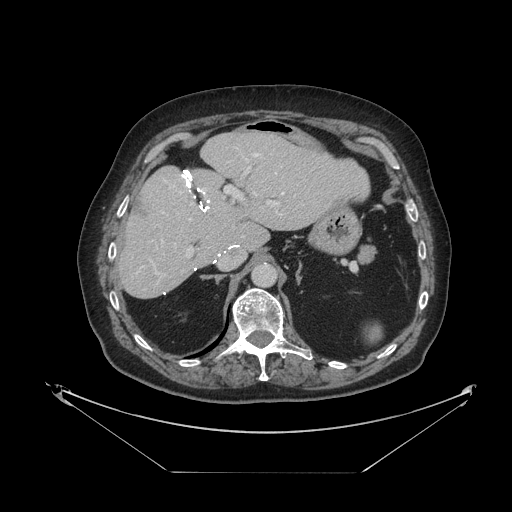
Contrast-enhanced abdominal CT, one axial slice. Position 69 of 121 along the scan axis. Reconstruction kernel STANDARD. 120 kVp. Intravenous contrast given. Soft-tissue window (W 400 / L 40 HU). 512 × 512 image matrix, field of view 500 × 500 mm. Male patient, age 68 years. Case-level facts recorded for this patient, not image findings: diagnosis: colorectal cancer liver metastases, imaged before liver resection; multiple liver metastases: no; largest metastasis: 4 cm.
Structures marked on this image (outlined manually by an expert reader):
- hepatic veins: bounding box [x1, y1, x2, y2] px = [162, 153, 284, 243]
- liver: [120, 133, 368, 299]
- planned liver remnant (the part of the liver to remain after resection): [120, 133, 368, 299]
- portal vein (with intrahepatic branches): [155, 168, 281, 274]
- liver metastasis: [131, 198, 149, 220]